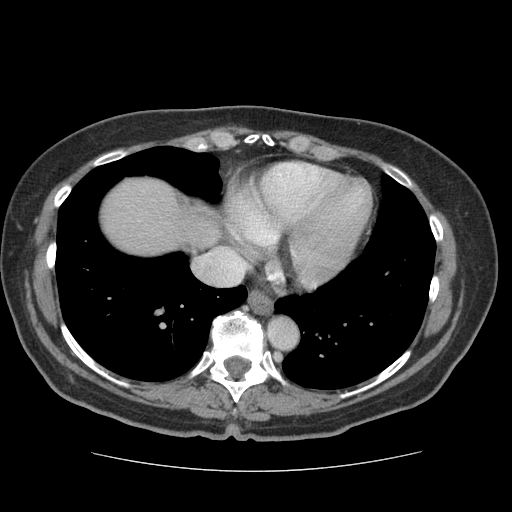
Contrast-enhanced abdominal CT (liver protocol), one axial slice; slice 68 of 75 in the series (ordered by position); 140 kVp; soft-tissue window (W 400 / L 40 HU); 2.5 mm slice thickness; 512 × 512 image matrix, field of view 360 × 360 mm. From the clinical record (not read from this slice): diagnosis: hepatocellular carcinoma (patient treated with transarterial chemoembolisation; whether this scan precedes or follows treatment is not stated here); TNM stage (as recorded): Stage-I.
Structures marked on this image (semi-automatic segmentation, software-assisted and operator-edited):
- liver parenchyma outside the tumour (the mass and vessels are separate outlines, so this box may not span the whole liver): bounding box <100,178,216,255> (left, top, right, bottom; pixels)